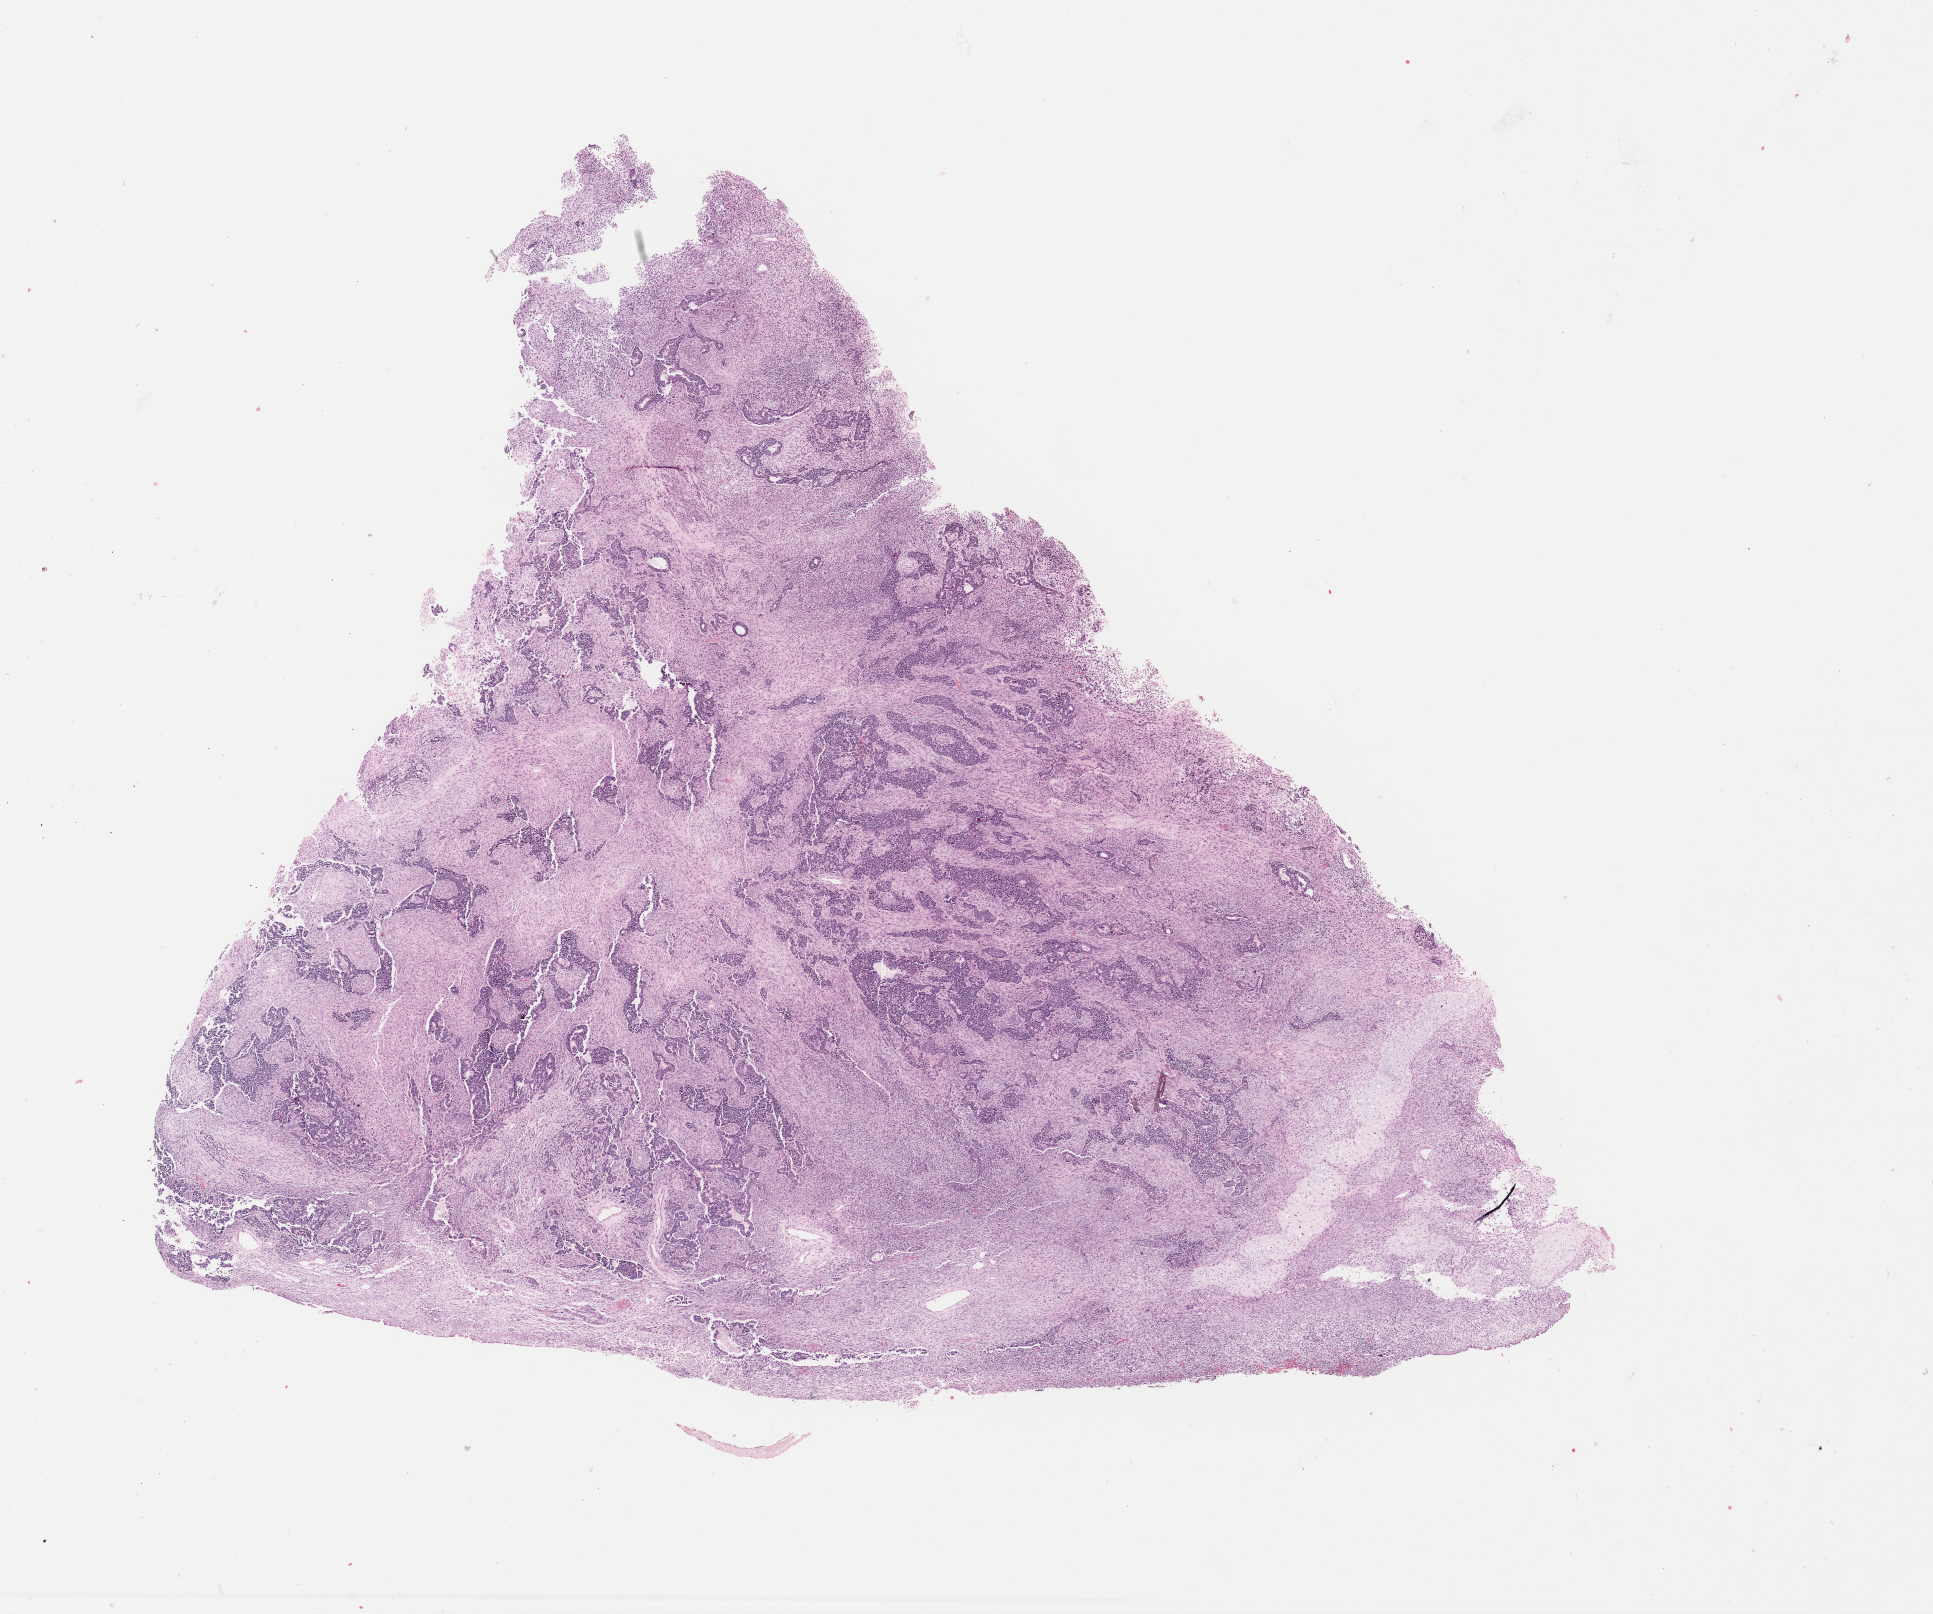
Whole-slide histology image, H&E-stained — shown as a low-resolution overview of the whole scanned area (about 15.3 x 12.8 mm, from a 40x scan), FFPE section, sample: primary tumour, uterus. Patient: female, age at initial diagnosis 77 years.
Lymph nodes positive (case pathology): 1 of 3 examined. Pathologic diagnosis: Mullerian mixed tumor. FIGO stage: IIIC2.